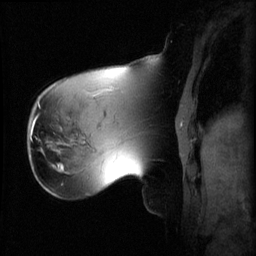
Breast MRI (dynamic contrast-enhanced), one sagittal slice; slice 17 of 60 in the series (ordered by position); 3 images stored at this slice position (order not interpretable as contrast timing); 1.5 T; TE 4.2 ms, TR 8.2 ms; 2.2 mm slice thickness; 256 × 256 image matrix, field of view 220 × 220 mm. Female patient, age 62 years.
Structures marked on this image (semi-automatically segmented with operator editing):
- analysis volume of interest (the breast-tissue region the enhancement analysis was run in; not a lesion): bounding box <28,126,59,165> (left, top, right, bottom; pixels)
- tumour enhancement mask (voxels above the 70 % enhancement threshold inside the analysis volume of interest): <30,126,35,141>